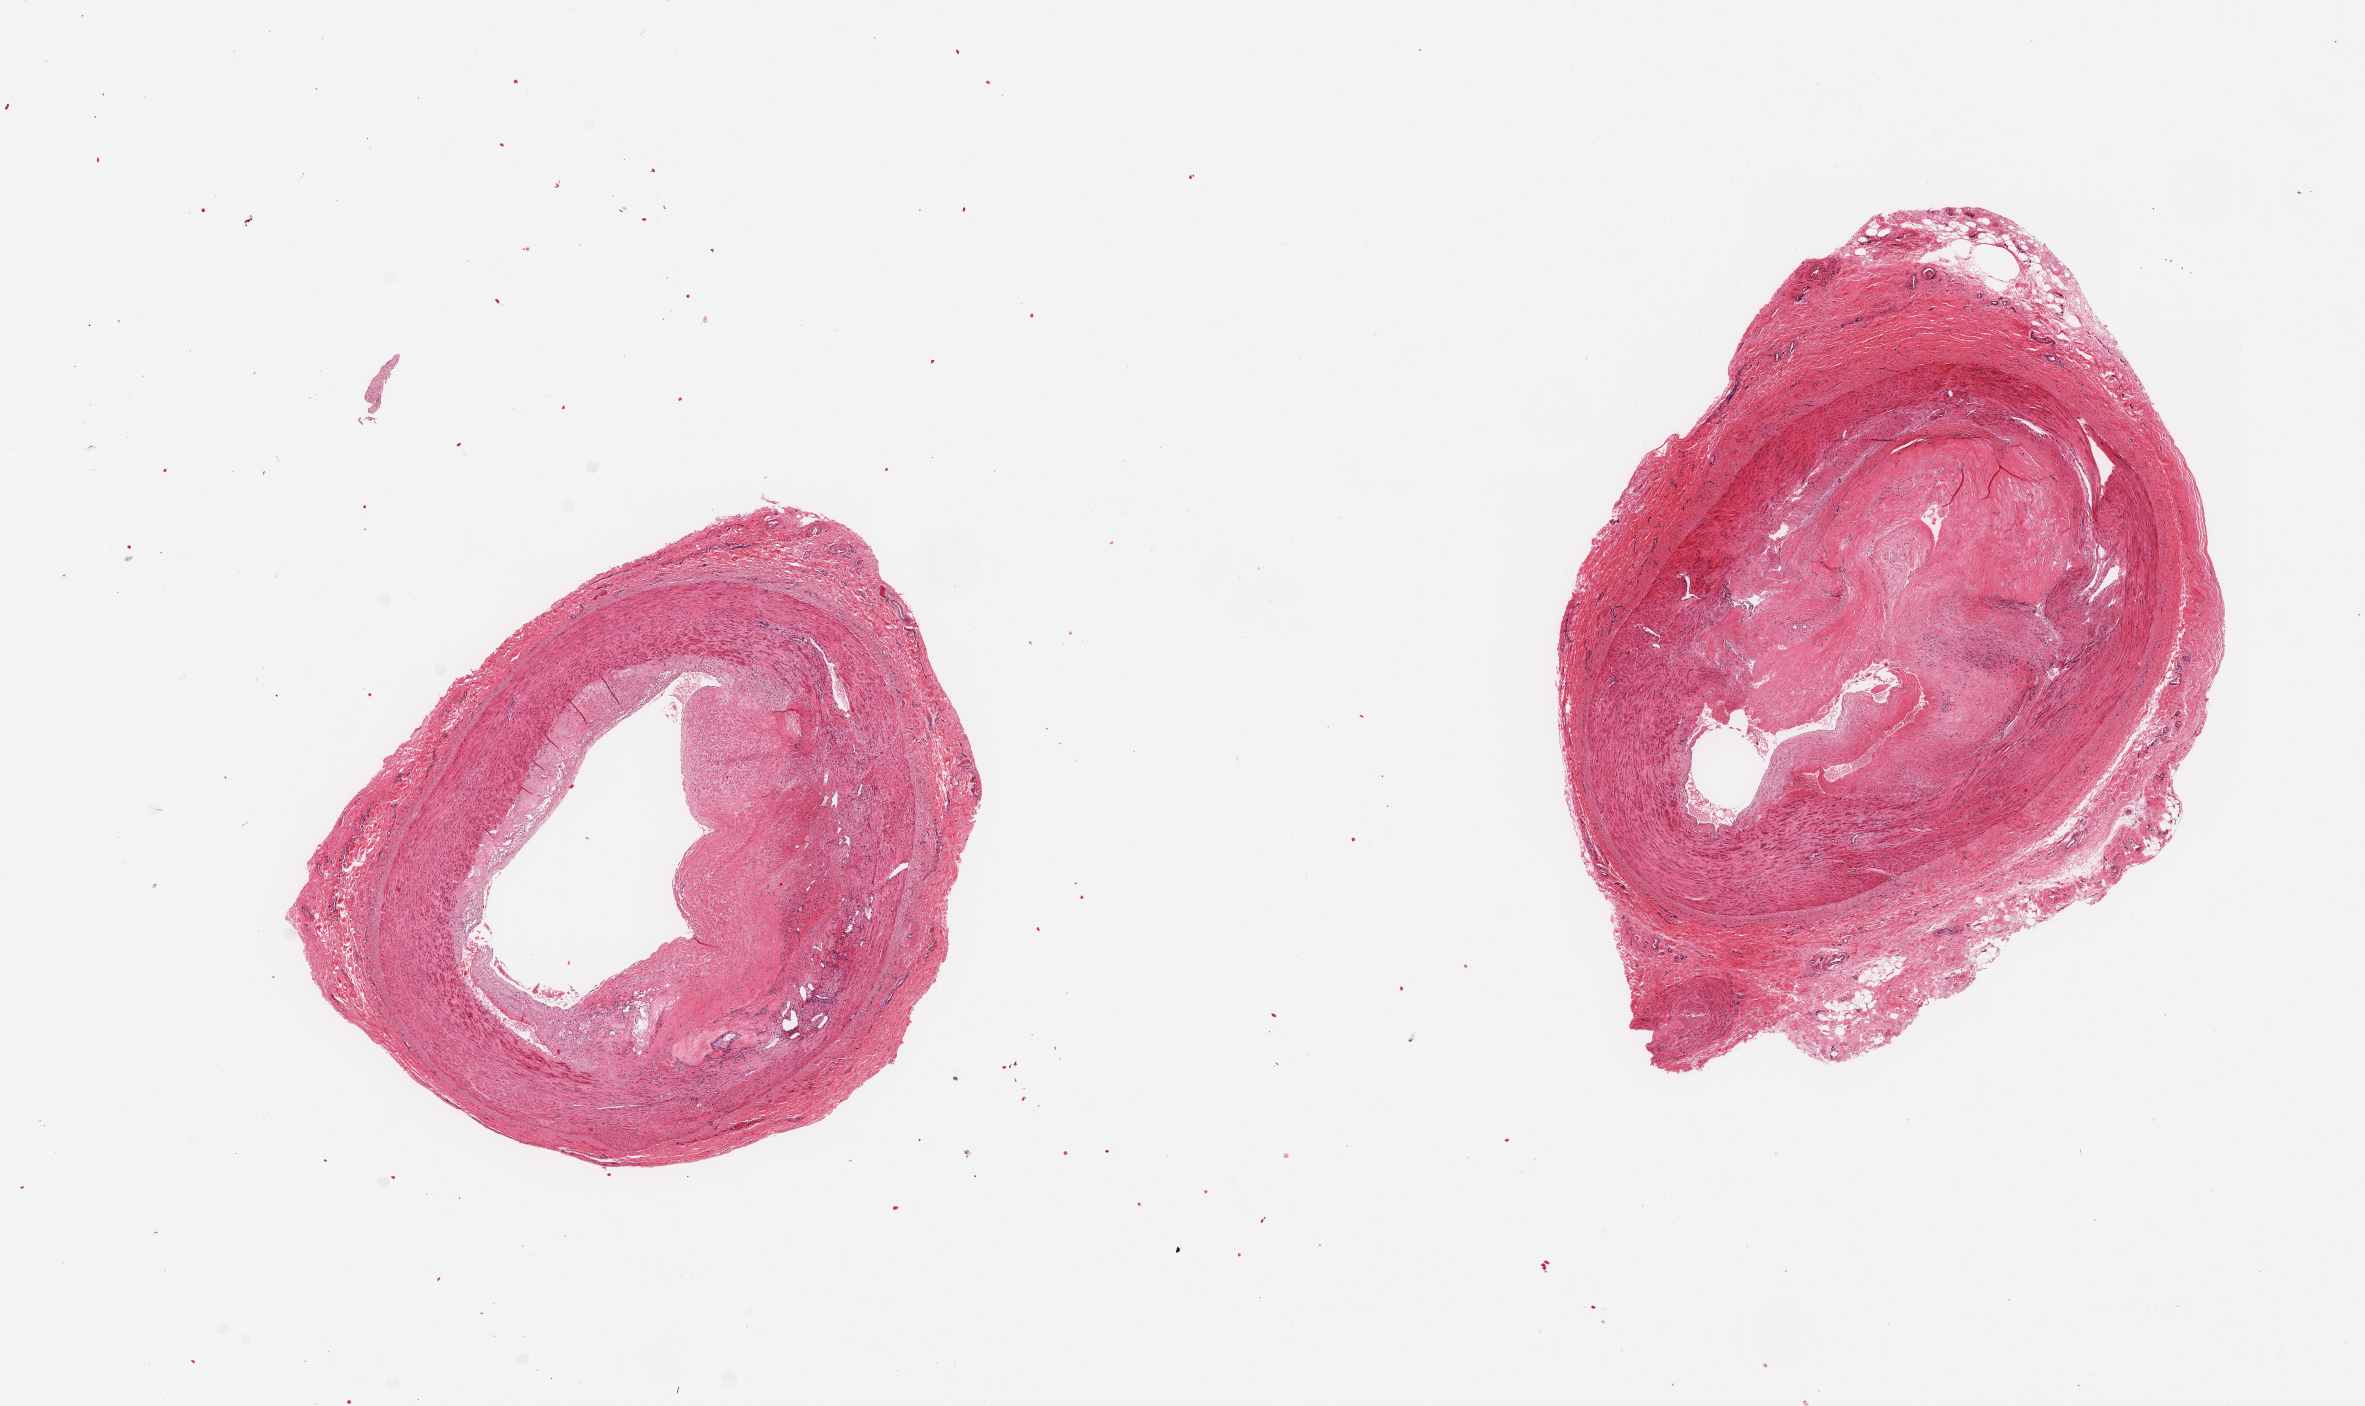
Whole-slide image, H&E stain, low-resolution overview of the scanned area, about 18.7 x 11.1 mm; PAXgene-fixed paraffin-embedded (PFPE) section; sampled site (target tissue): tibial artery; tissue donor sample.
Reviewer comment on this tissue sample: 2 pieces, subtotally occlusive atherosis.